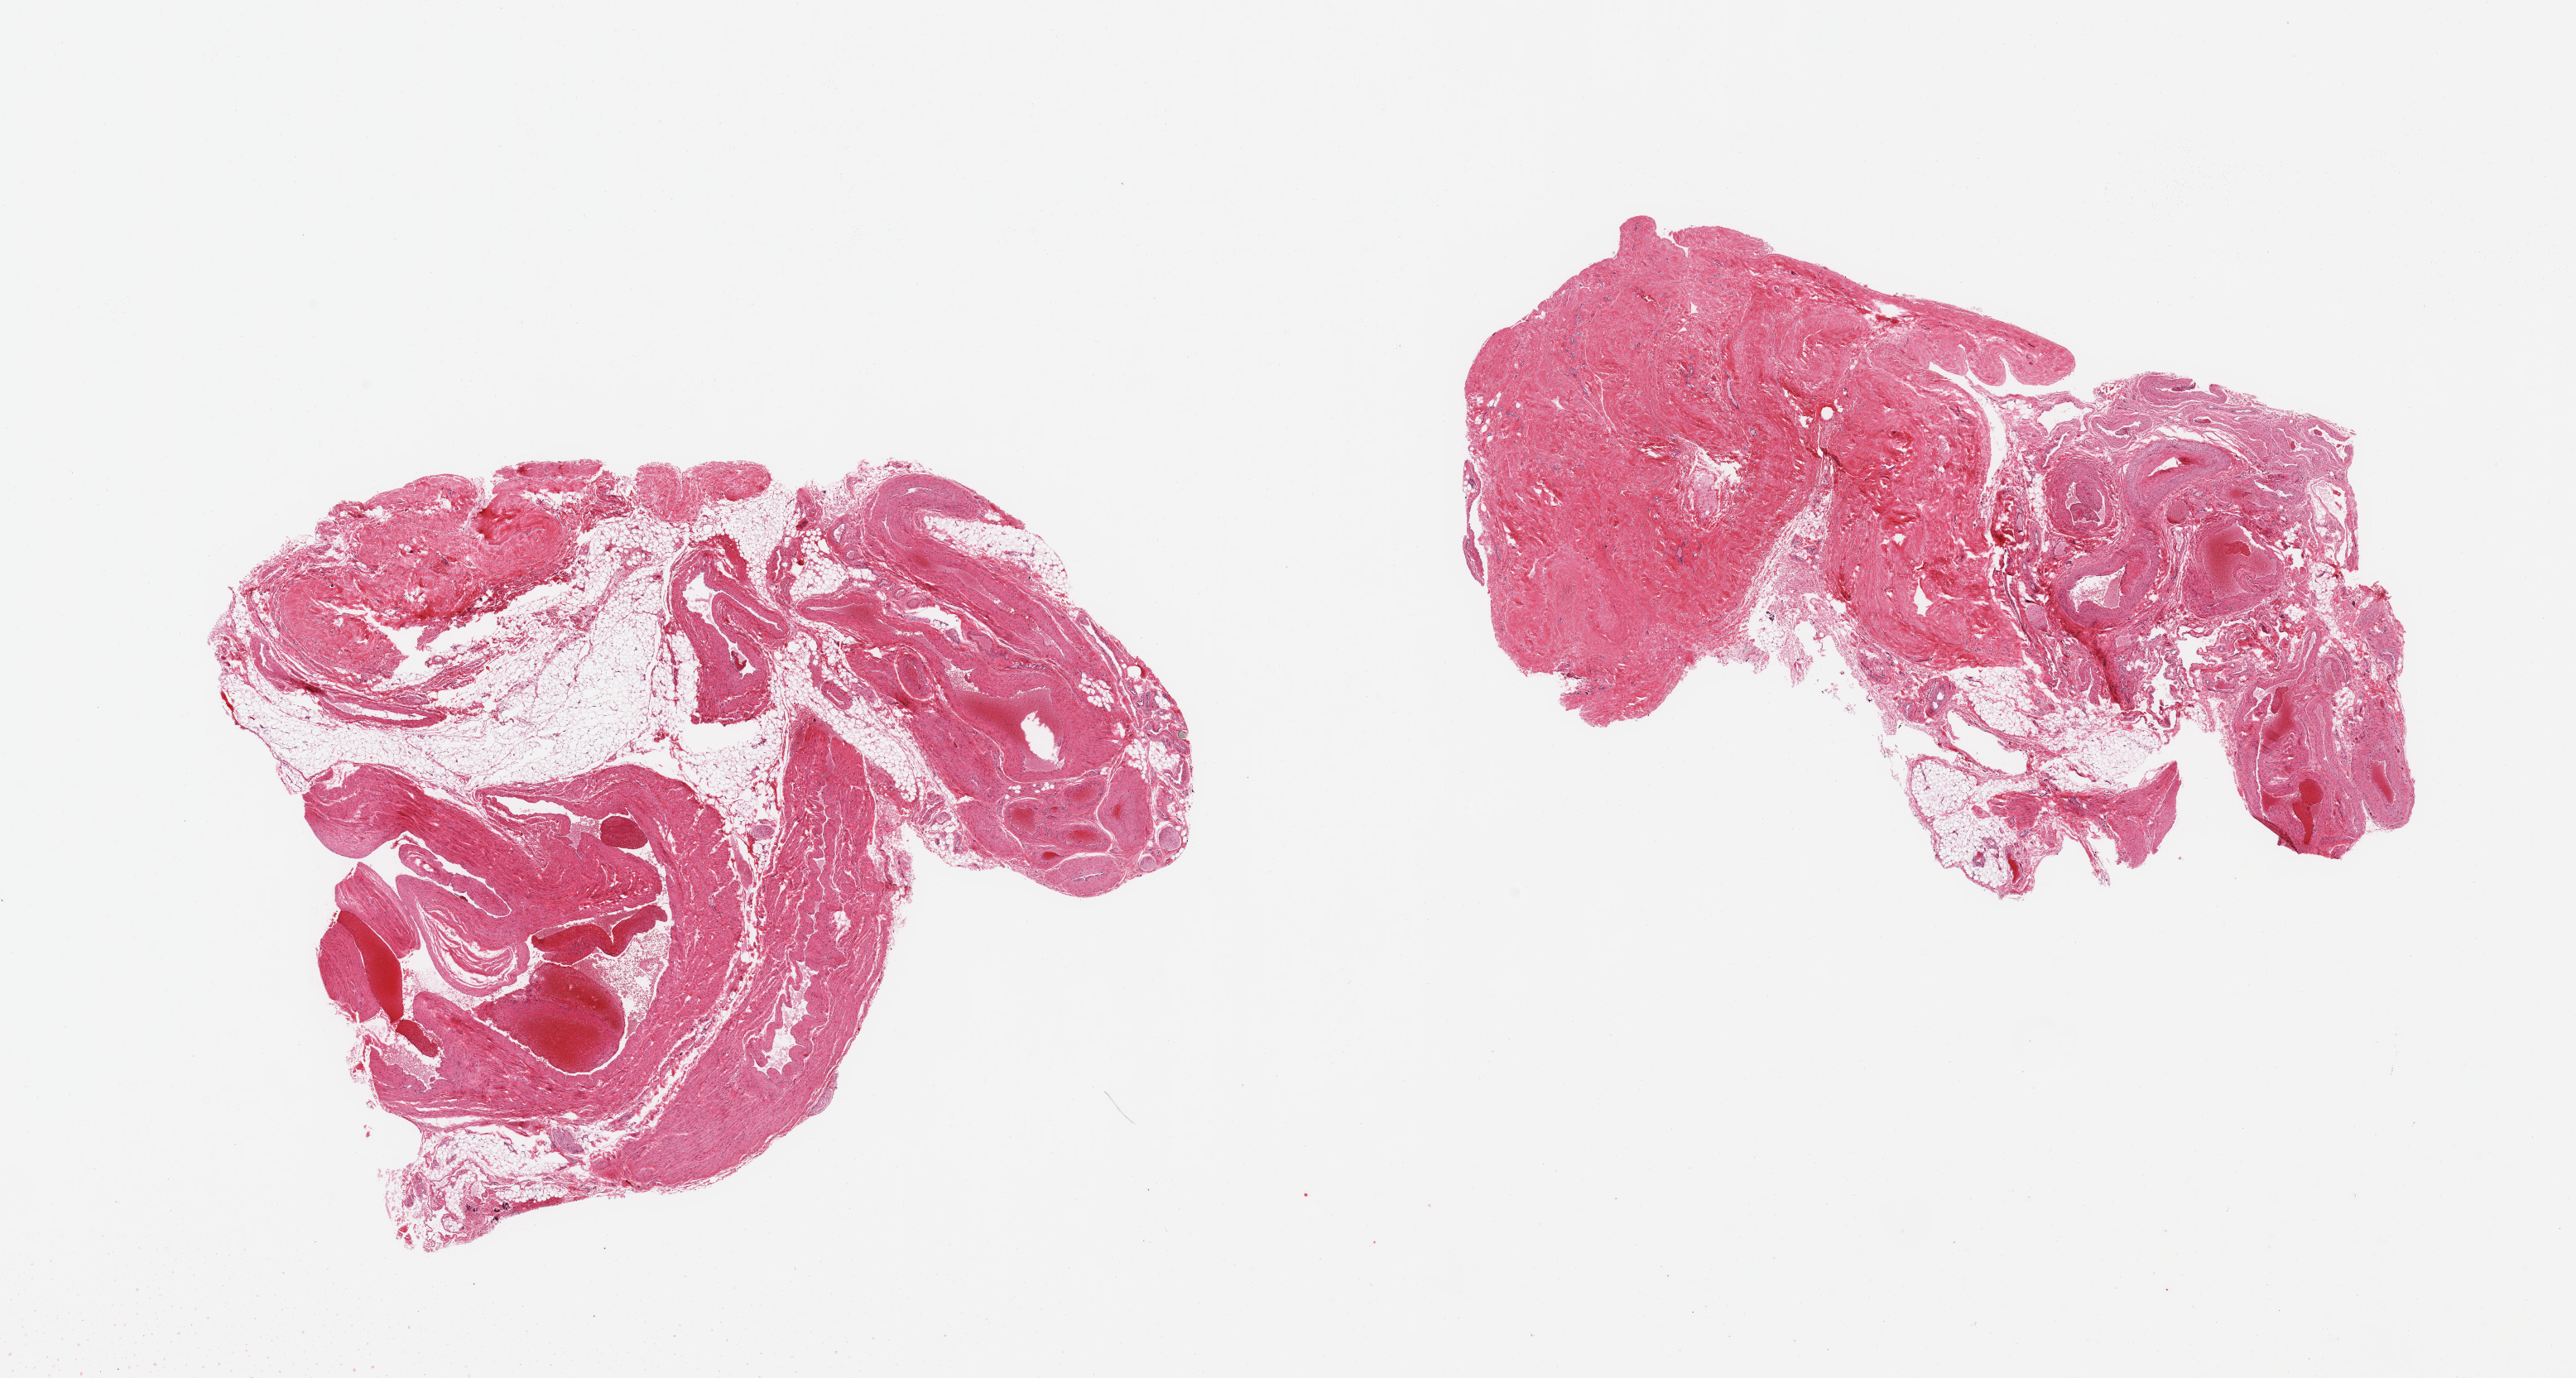
H&E whole-slide image, brightfield — shown as a low-resolution overview of the whole scanned area (about 24.6 x 13.2 mm, slide scanned at 20x). PAXgene-fixed, paraffin-embedded tissue. Target tissue: ovary. Donor tissue sample. Donor: female.
Reviewer comment on this tissue sample: 2 pieces, no ovarian tissue, fibroadipose tissue.